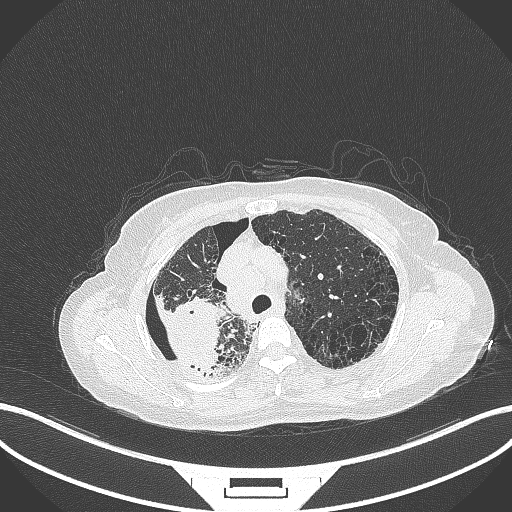
Chest CT, one axial slice; slice 267 of 408 in the series (ordered by position); reconstruction kernel B70f; lung window (W 1500 / L -600 HU); 1 mm slice thickness; 512 × 512 image matrix, field of view 400 × 400 mm. Female patient, age 64 years. Case-level facts recorded for this patient, not image findings: clinical TNM (as recorded): T3 N3 M0.
Outlined on this slice (bounding box drawn by a radiologist):
- lung tumour (recorded histology: squamous cell carcinoma): bounding box <154,291,224,375> (left, top, right, bottom; pixels)